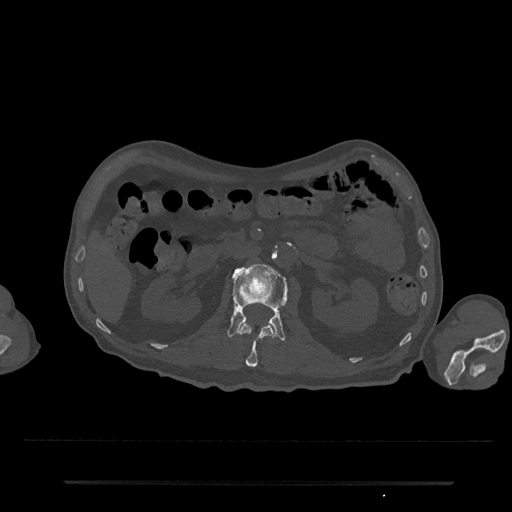
CT including the spine, one axial slice; slice 90 of 797 in the series (ordered by position); 120 kVp; bone window (W 1800 / L 400 HU); 0.5 mm slice thickness; 512 × 512 image matrix, field of view 427 × 427 mm. Male patient, age 74 years. From the clinical record (not read from this slice): primary cancer: prostate.
Annotated regions visible in this slice (semi-automatically segmented with operator editing):
- L1 vertebra: box from (x=239, y=323) to (x=274, y=367) px
- L2 vertebra: (x=227, y=263)–(x=288, y=341)